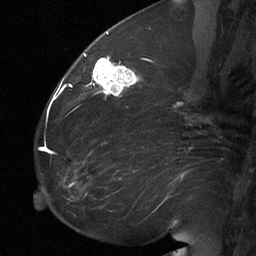
Breast MRI (dynamic contrast-enhanced), one sagittal slice; position 27 of 64 along the scan axis; dynamic contrast-enhanced study with each time point stored as its own series, time point 2 of 3 at this slice position (early post-contrast, ordered by acquisition time); 1.5 T; TE 4.8 ms, TR 27 ms; 256 × 256 image matrix, field of view 200 × 200 mm. Patient: female, 60 years. From the clinical record (not read from this slice): setting: breast cancer imaged before/during neoadjuvant chemotherapy; receptor status: HR-positive, HER2-negative.
Structures marked on this image (semi-automatic segmentation, software-assisted and operator-edited):
- analysis volume of interest (the breast-tissue region the enhancement analysis was run in; not a lesion): bounding box [x1, y1, x2, y2] px = [91, 56, 139, 103]
- tumour enhancement mask (voxels above the 90 % enhancement threshold inside the analysis volume of interest): [93, 57, 139, 95]